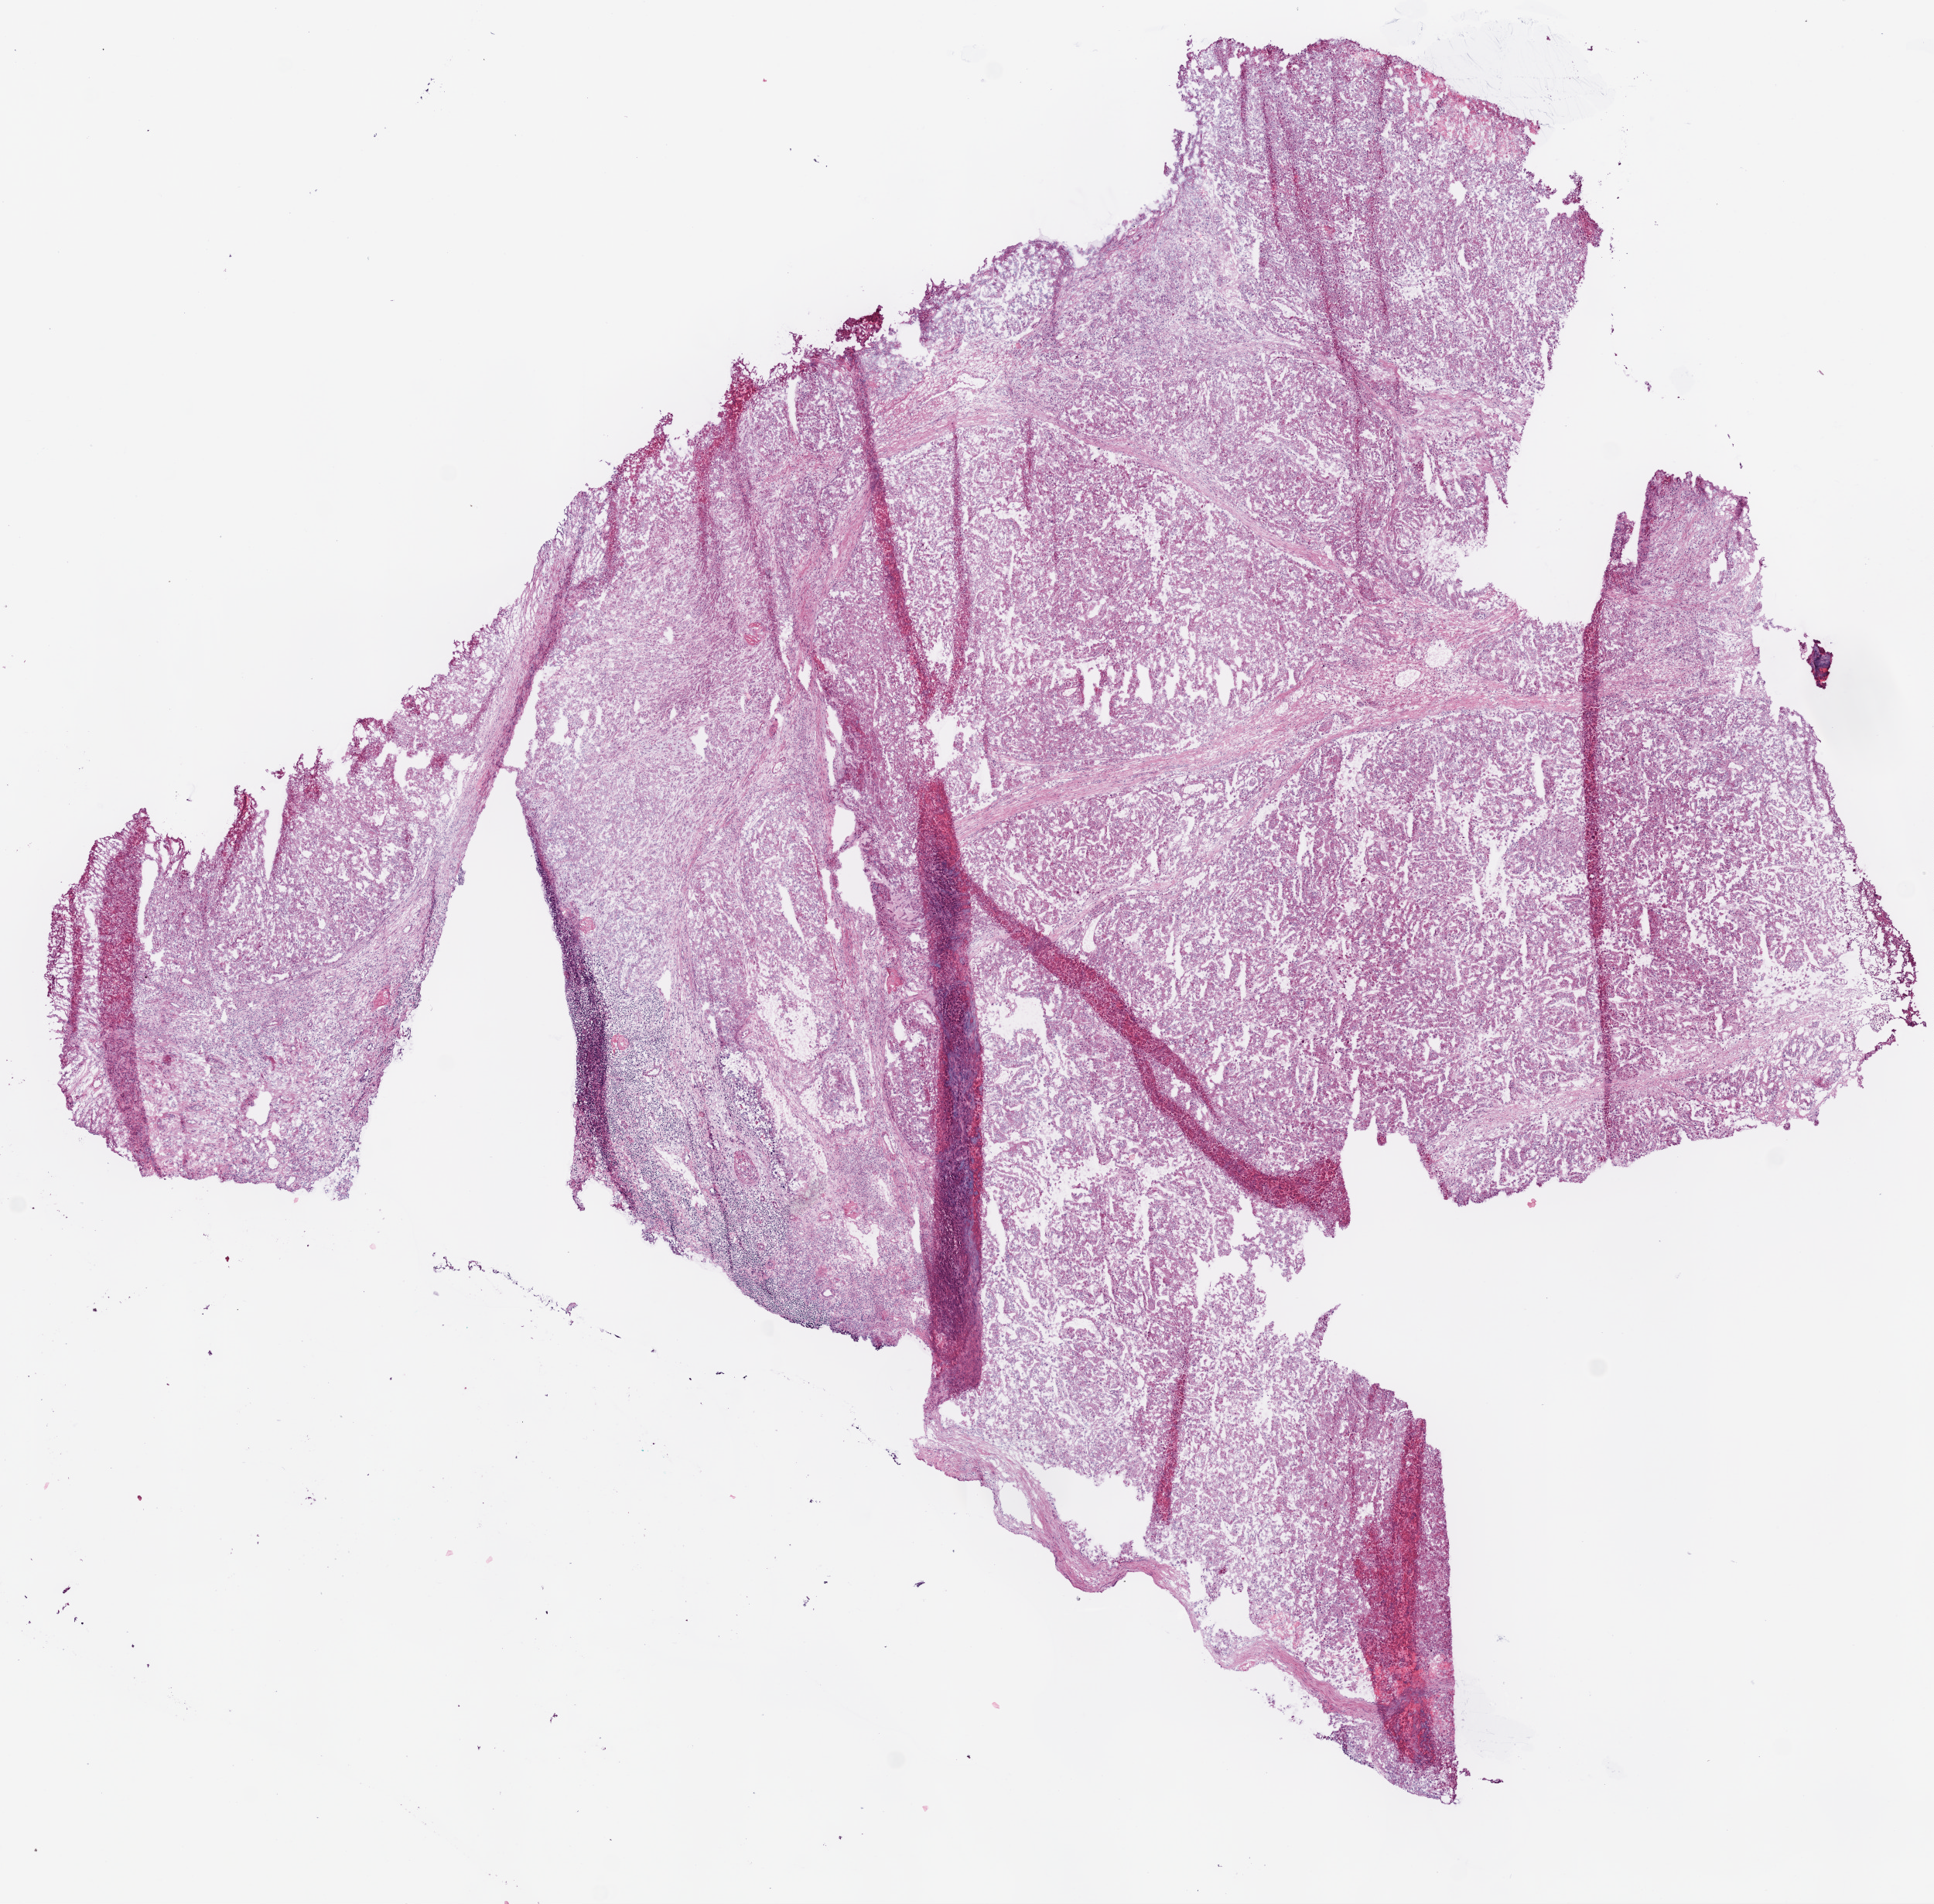
H&E-stained whole-slide image, a low-resolution overview of the entire scanned area, about 10.0 x 9.9 mm (slide scanned at 20x). Frozen section. Sample: primary tumour, kidney. Male, age 41 years at initial diagnosis. Composition of this section per pathologist review: tumour cells 87%, tumour nuclei 75%.
Pathologic diagnosis: Papillary adenocarcinoma, NOS.